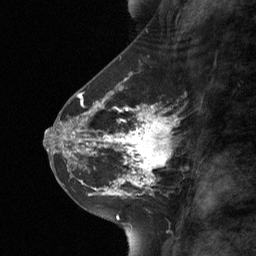
Breast MRI (dynamic contrast-enhanced), one sagittal slice. Position 29 of 64 along the scan axis. Dynamic contrast-enhanced study with each time point stored as its own series, time point 2 of 3 at this slice position (early post-contrast, ordered by acquisition time). 1.5 T. TE 4.8 ms, TR 27 ms. 2 mm slice thickness. 256 × 256 image matrix, field of view 180 × 180 mm. Female patient, age 42 years. From the clinical record (not read from this slice): setting: breast cancer imaged before/during neoadjuvant chemotherapy; receptor status: triple-negative.
Outlined on this slice (semi-automatically segmented with operator editing):
- analysis volume of interest (the breast-tissue region the enhancement analysis was run in; not a lesion): bounding box (x1, y1, x2, y2) in pixels: (111, 107, 174, 178)
- tumour enhancement mask (voxels above the 90 % enhancement threshold inside the analysis volume of interest): (111, 113, 169, 178)